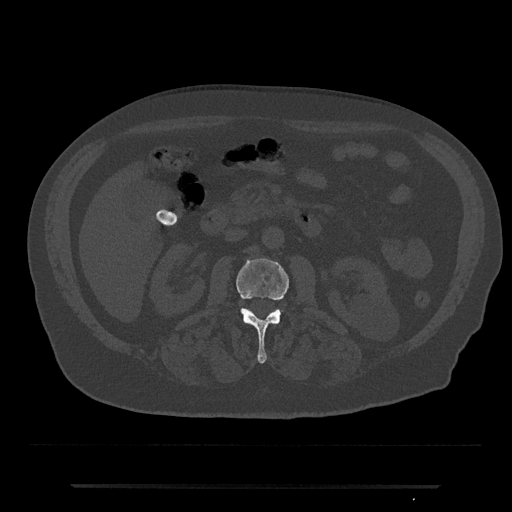
CT including the spine, one axial slice. Bone window (W 1800 / L 400 HU). 0.5 mm slice thickness. 512 × 512 image matrix, field of view 434 × 434 mm. Patient: male, 80 years. Case-level facts recorded for this patient, not image findings: primary cancer: prostate; vertebrae with lytic lesions (as recorded): L1, T11.
Annotated regions visible in this slice (semi-automatically segmented with operator editing):
- L2 vertebra: bounding box <236,258,289,363> (left, top, right, bottom; pixels)